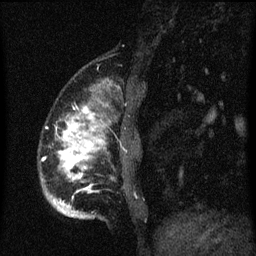
Breast MRI (dynamic contrast-enhanced), one sagittal slice; position 15 of 60 along the scan axis; dynamic contrast-enhanced series, image 2 of 3 at this slice position (ordered by acquisition); 1.5 T; TE 4.2 ms, TR 8.4 ms; 2 mm slice thickness; 256 × 256 image matrix. Female patient, age 34 years. Case-level facts recorded for this patient, not image findings: setting: breast cancer imaged before/during neoadjuvant chemotherapy; receptor status: HR-positive, HER2-negative.
Outlined on this slice (semi-automatically segmented with operator editing):
- analysis volume of interest (the breast-tissue region the enhancement analysis was run in; not a lesion): bounding box (x1, y1, x2, y2) in pixels: (40, 78, 143, 221)
- tumour enhancement mask (voxels above the 70 % enhancement threshold inside the analysis volume of interest): (60, 108, 105, 193)